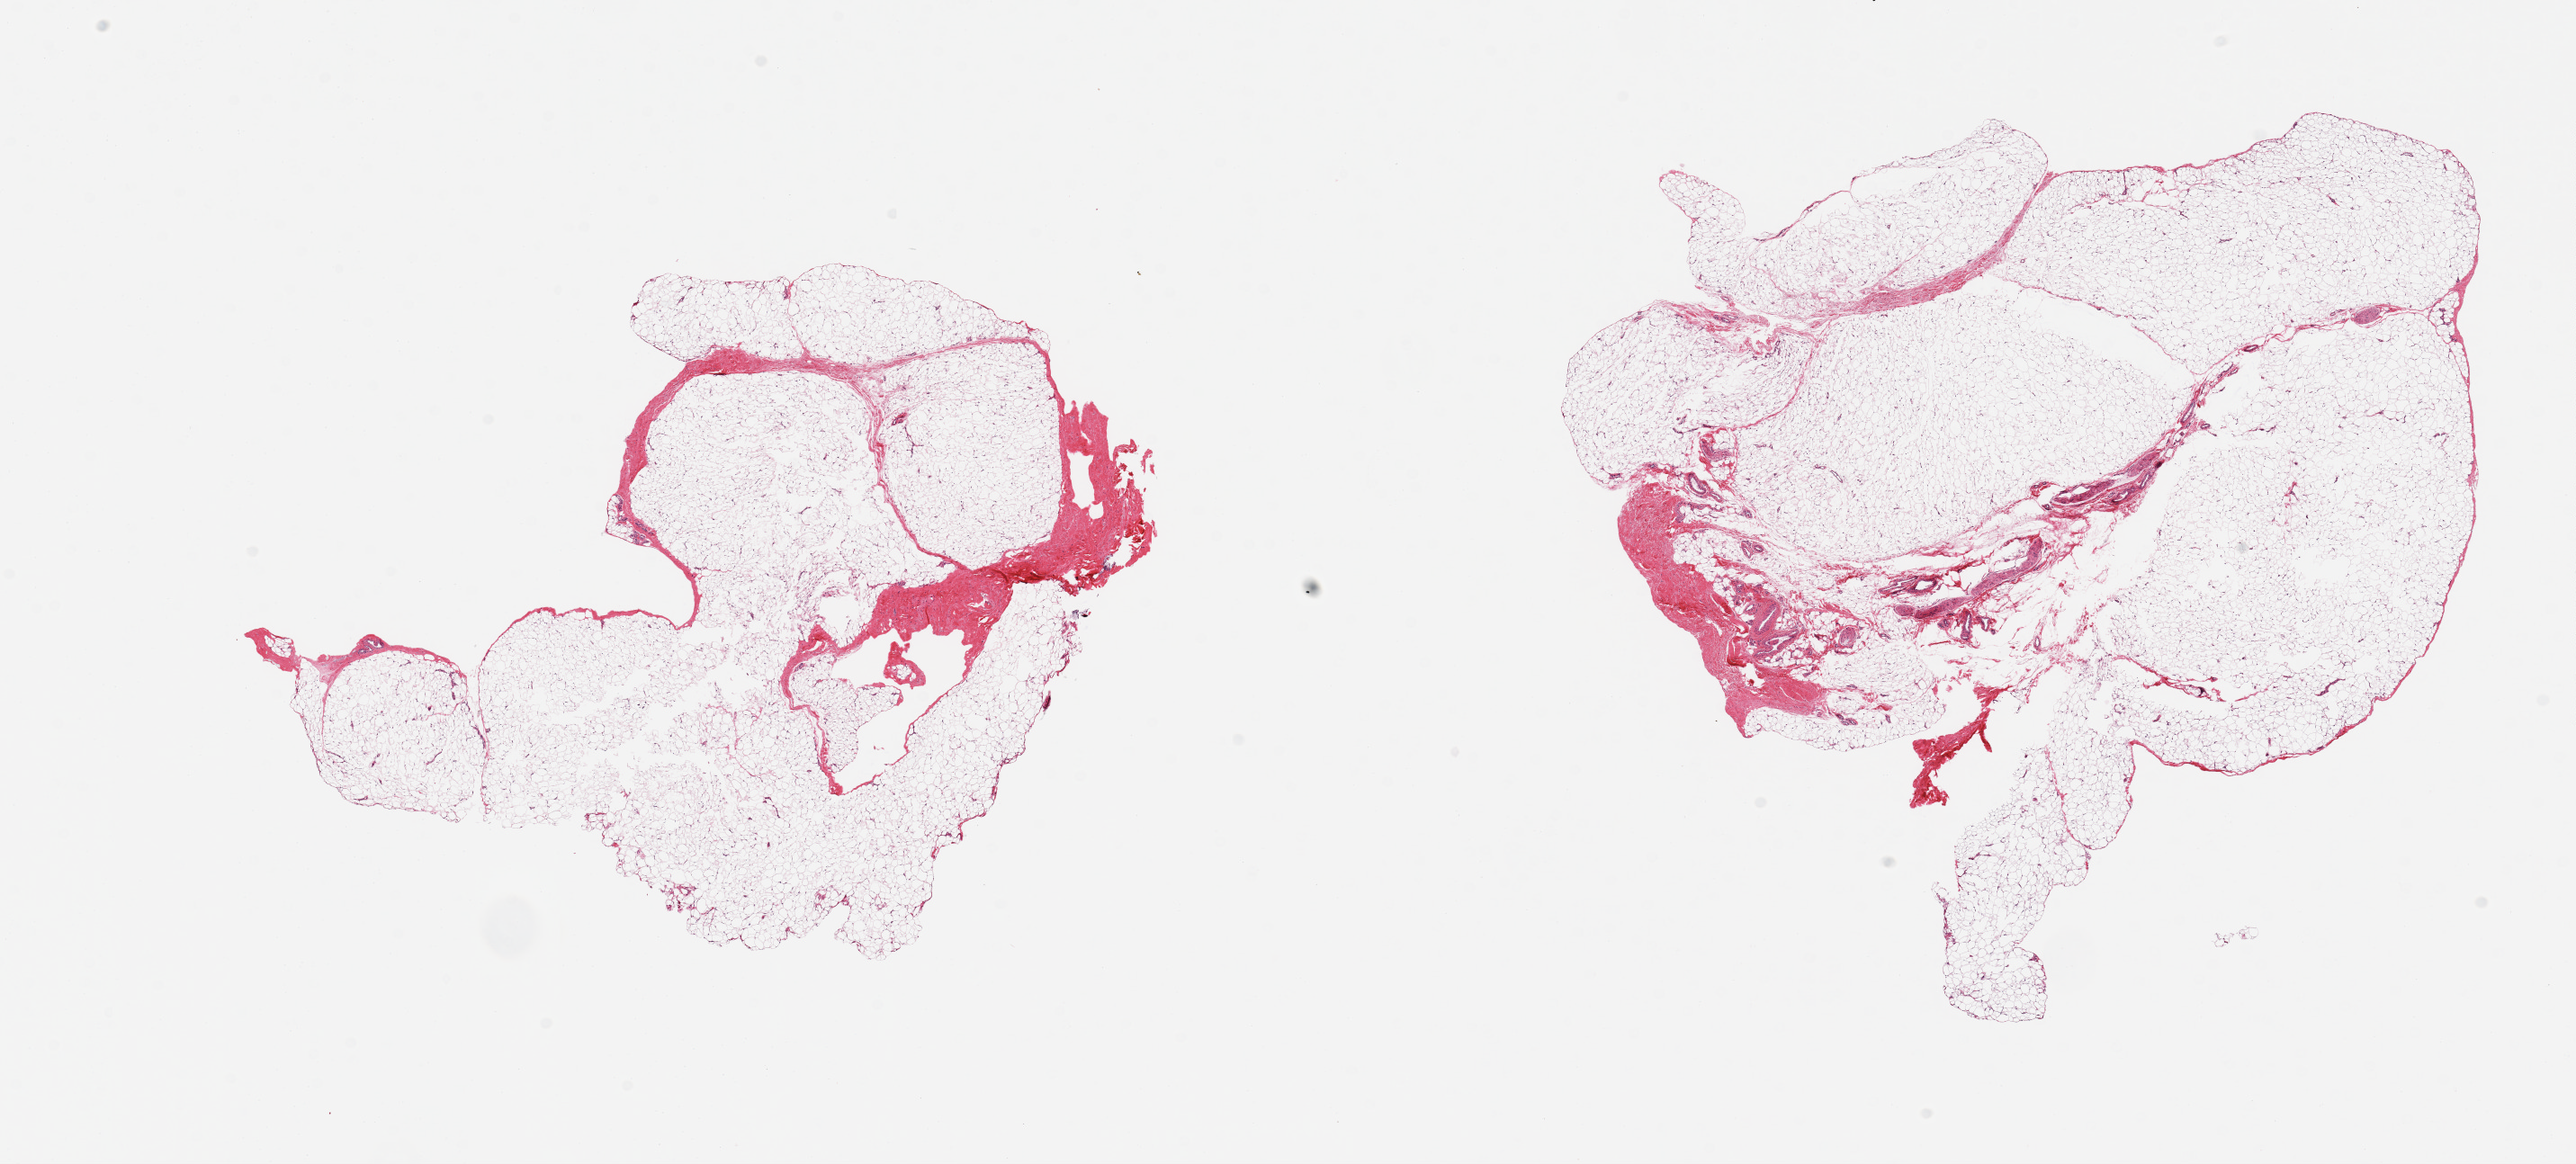
H&E whole-slide image — a low-resolution overview of the entire scanned area, about 22.6 x 10.2 mm. PAXgene-fixed paraffin-embedded (PFPE) section. Target tissue: adipose tissue. Donor tissue sample. Donor: male.
Review note (as recorded): 2 pieces; fat with 5-10% dense fibrous tissue/vessels/nerve.